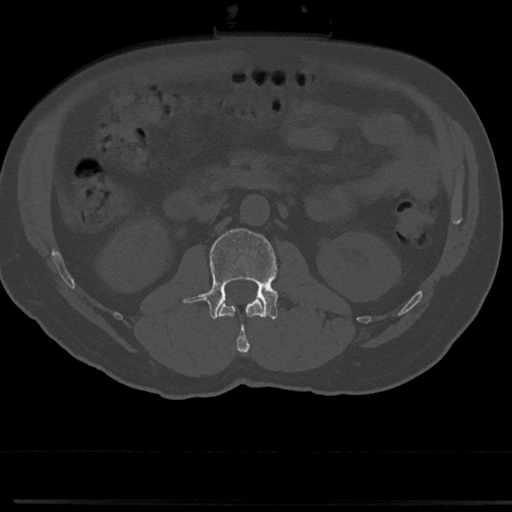
CT including the spine, one axial slice. Slice 34 of 817 in the series (ordered by position). Reconstruction kernel Br40s/3. Bone window (W 1800 / L 400 HU). 0.5 mm slice thickness. 512 × 512 image matrix, field of view 355 × 355 mm. Patient: male, 61 years. Case-level facts recorded for this patient, not image findings: primary cancer: prostate.
Structures marked on this image (semi-automatic segmentation, software-assisted and operator-edited):
- L1 vertebra: box from (x=219, y=299) to (x=263, y=355) px
- L2 vertebra: (x=191, y=228)–(x=278, y=319)